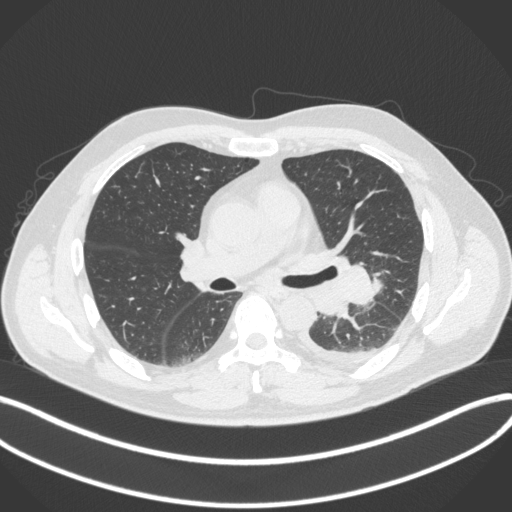
Chest CT, one axial slice. Position 208 of 350 along the scan axis. Reconstruction kernel B31f. Lung window (W 1500 / L -600 HU). 1 mm slice thickness. 512 × 512 image matrix, field of view 400 × 400 mm. Patient: male, 58 years. From the clinical record (not read from this slice): clinical TNM (as recorded): T3 N1 M1b.
Annotated regions visible in this slice (bounding box drawn by a radiologist):
- lung tumour (recorded histology: small cell carcinoma): bounding box (x1, y1, x2, y2) in pixels: (306, 261, 380, 319)